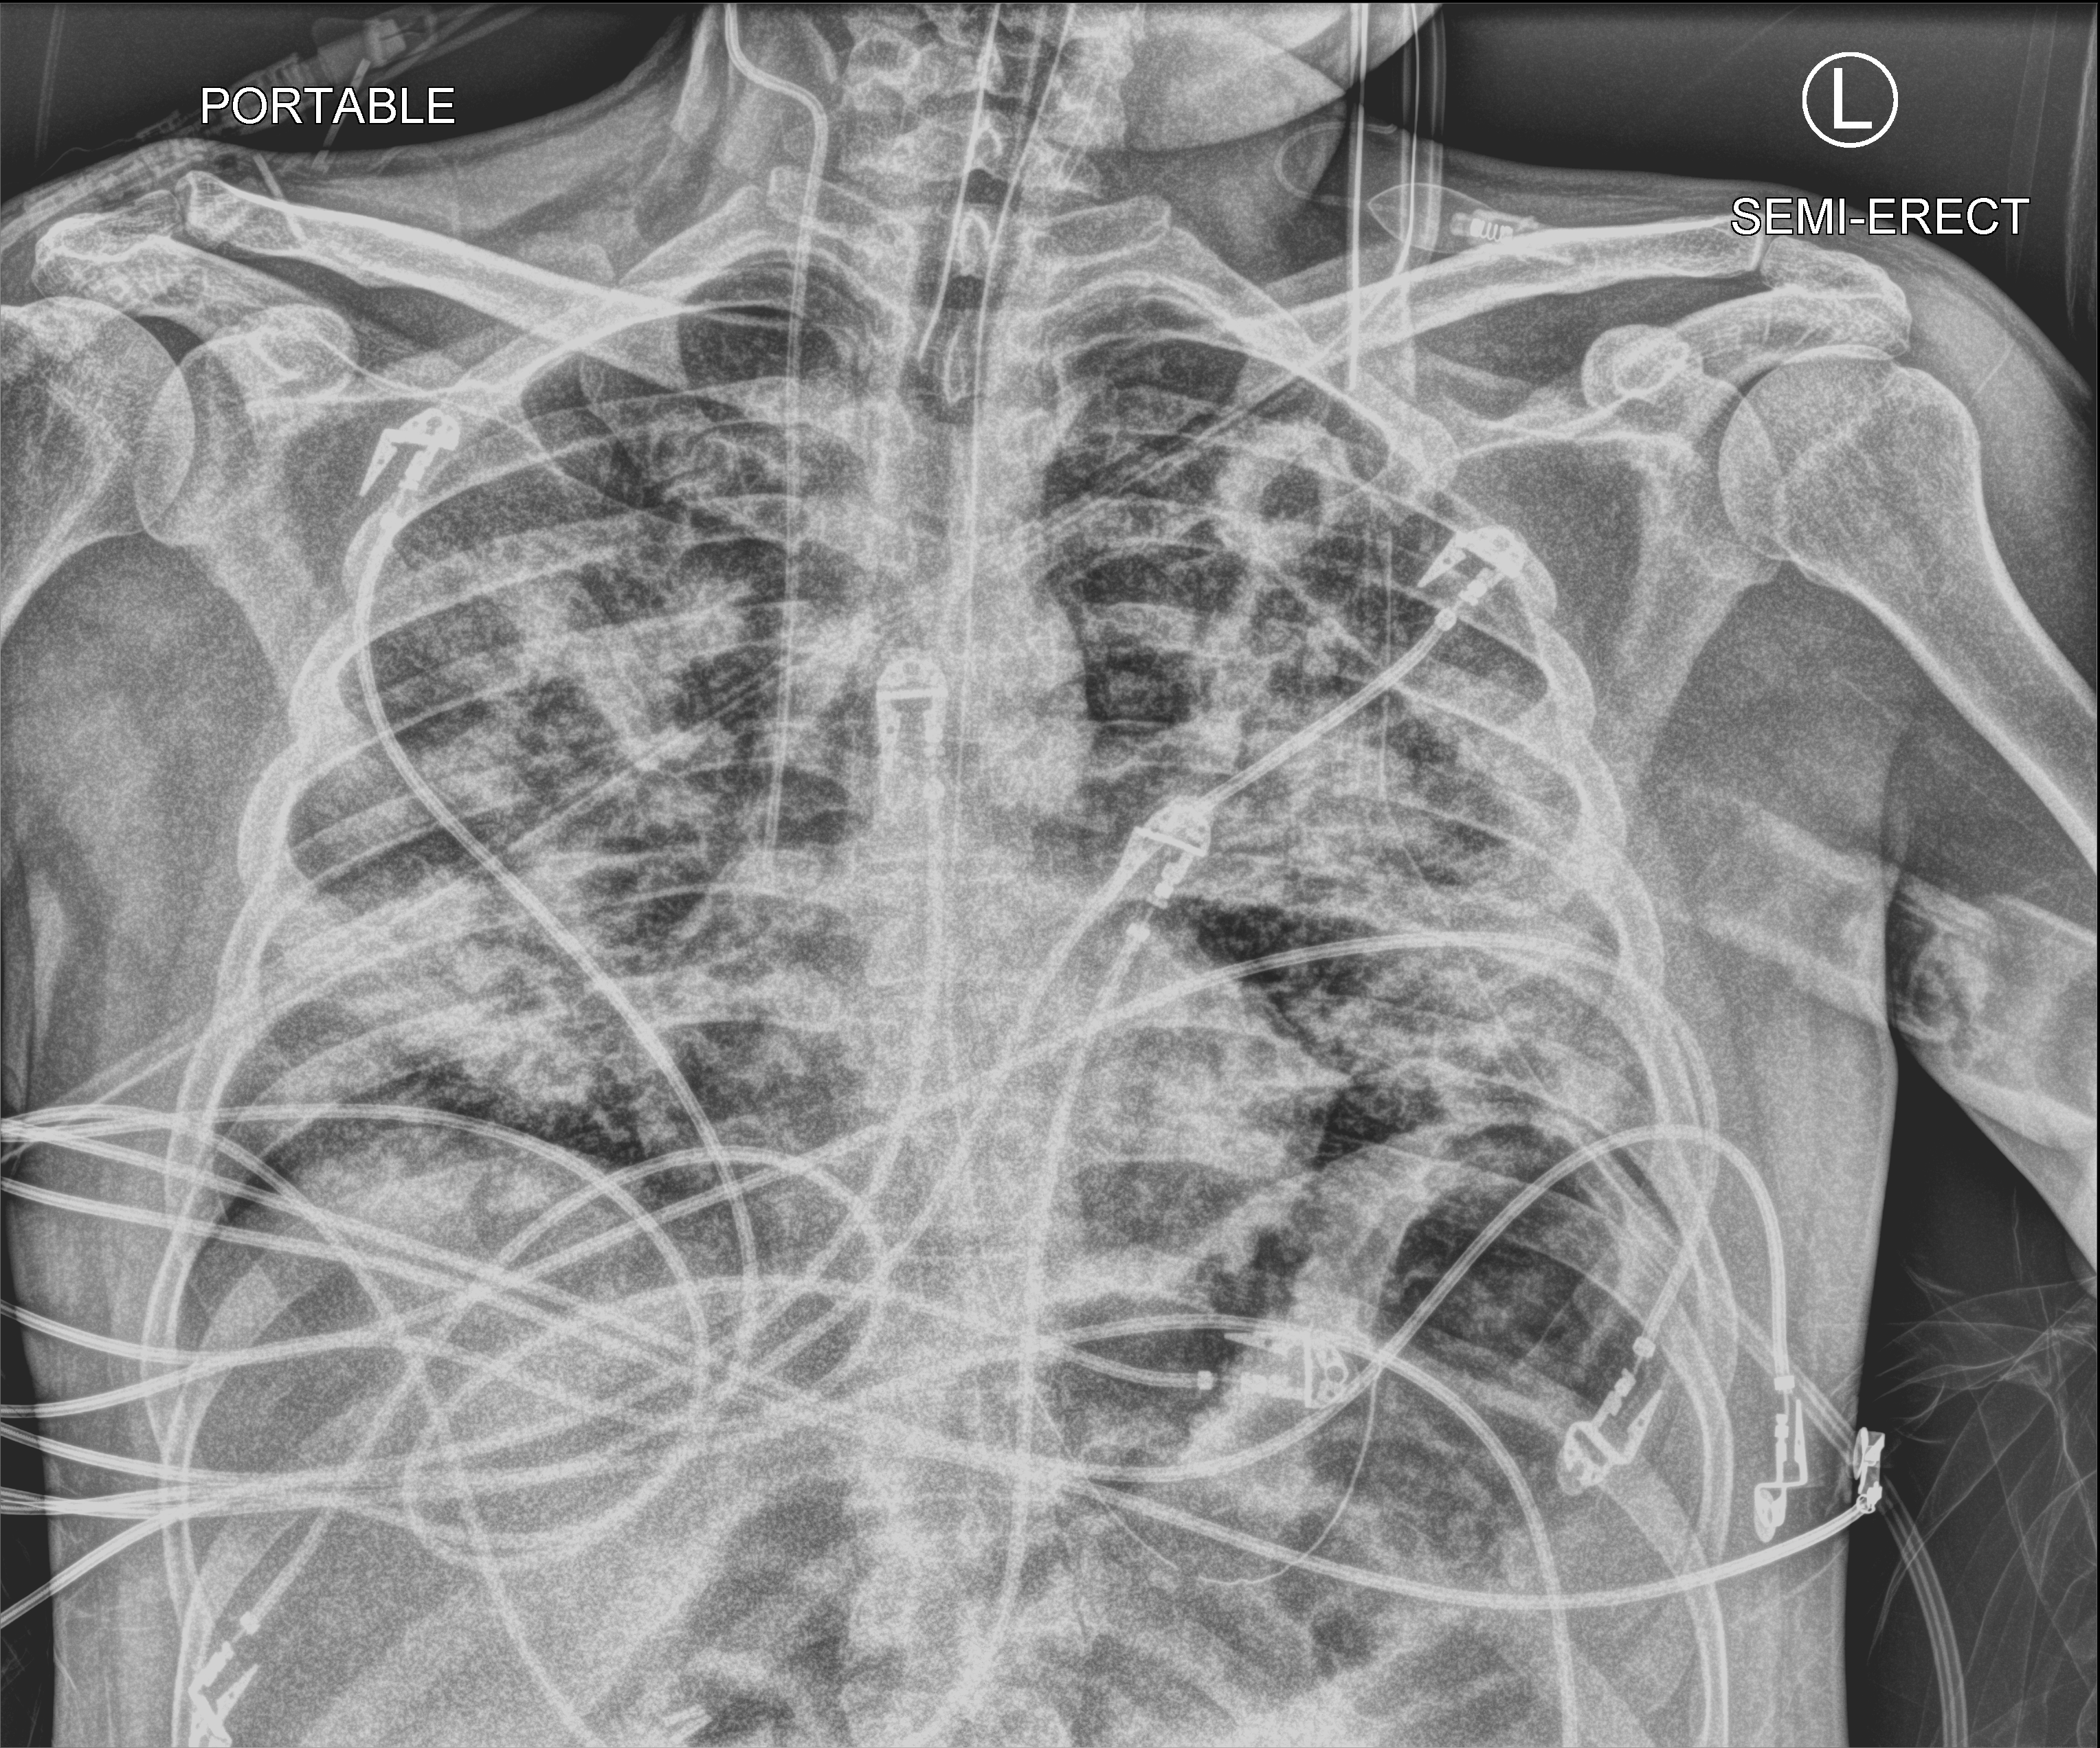
Chest X-ray (portable). Patient hospitalised with COVID-19; male, aged 18–59 years.
Hospital-stay facts (about this admission, not read from this image; timing relative to this image not recorded):
- admitted to intensive care during this hospital stay: yes